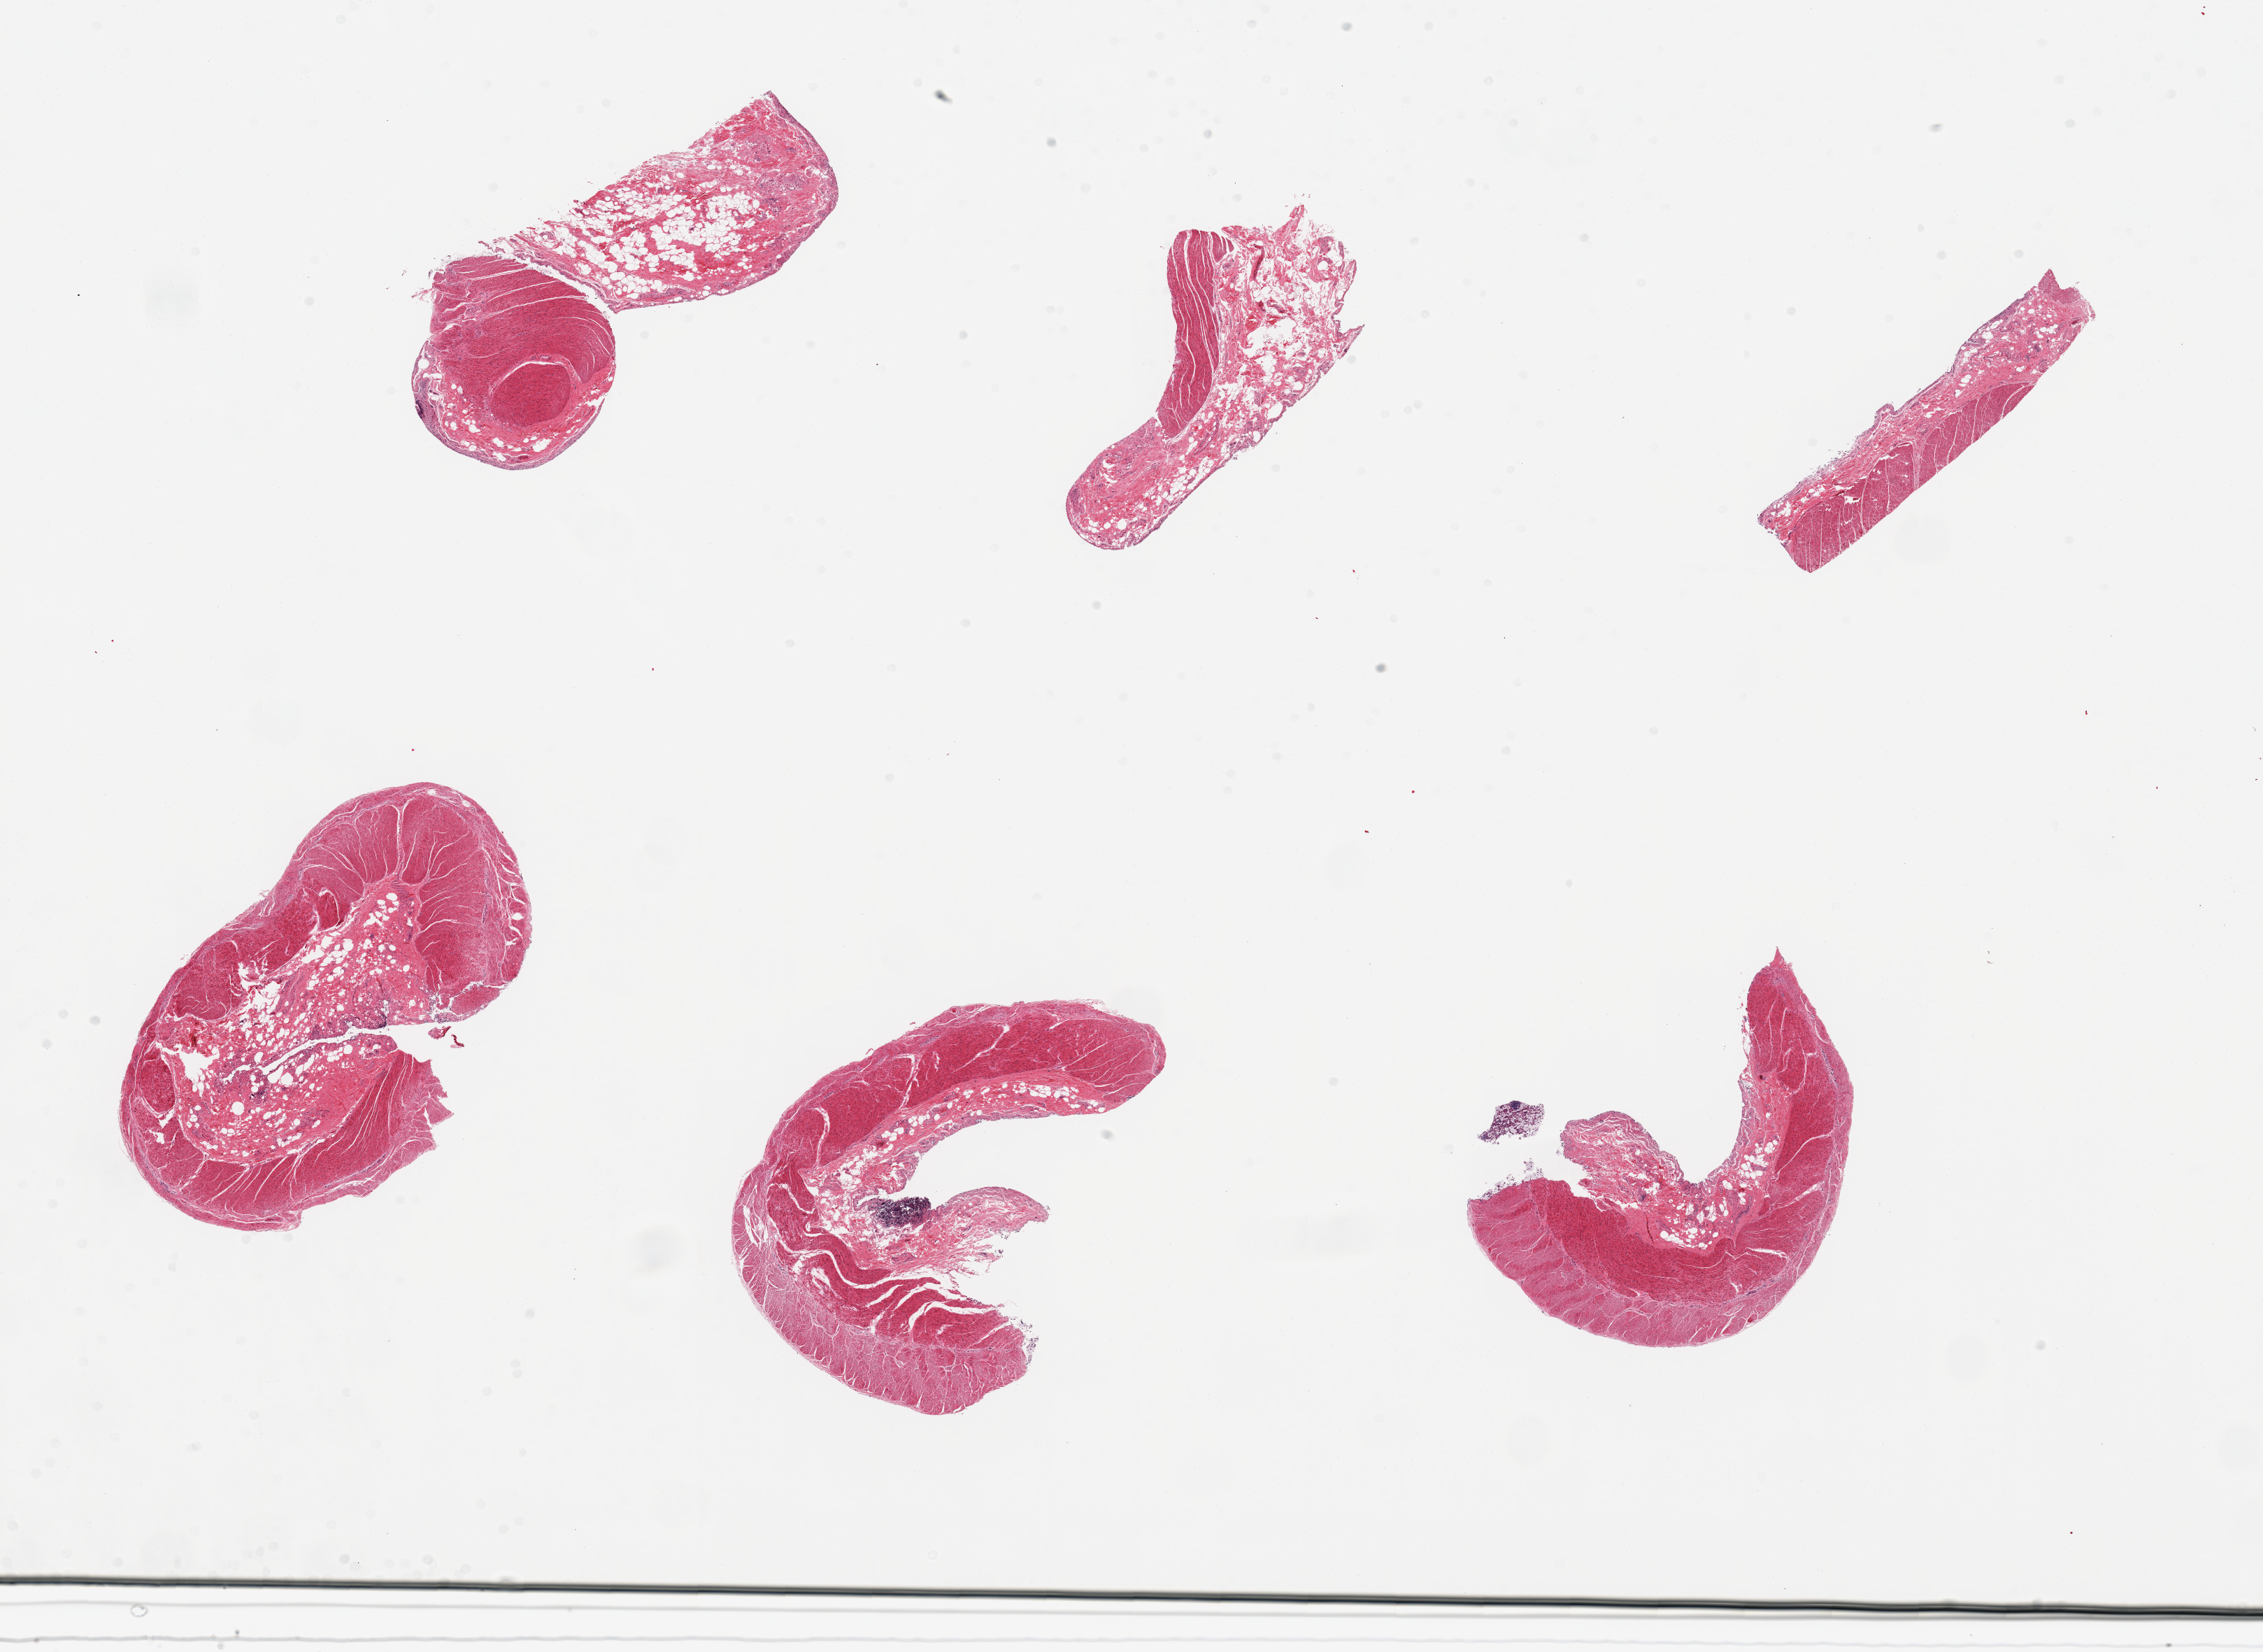
Digitized hematoxylin and eosin (H&E)-stained section, shown as a low-resolution overview of the whole scanned area (about 25.6 x 18.7 mm). PAXgene-fixed paraffin-embedded (PFPE) section. Target tissue: sigmoid colon. Donor tissue sample. Donor: male.
Reviewer comment on this tissue sample: 6 pieces; excessive perimuscular fibrofatty tissue; muscularis.